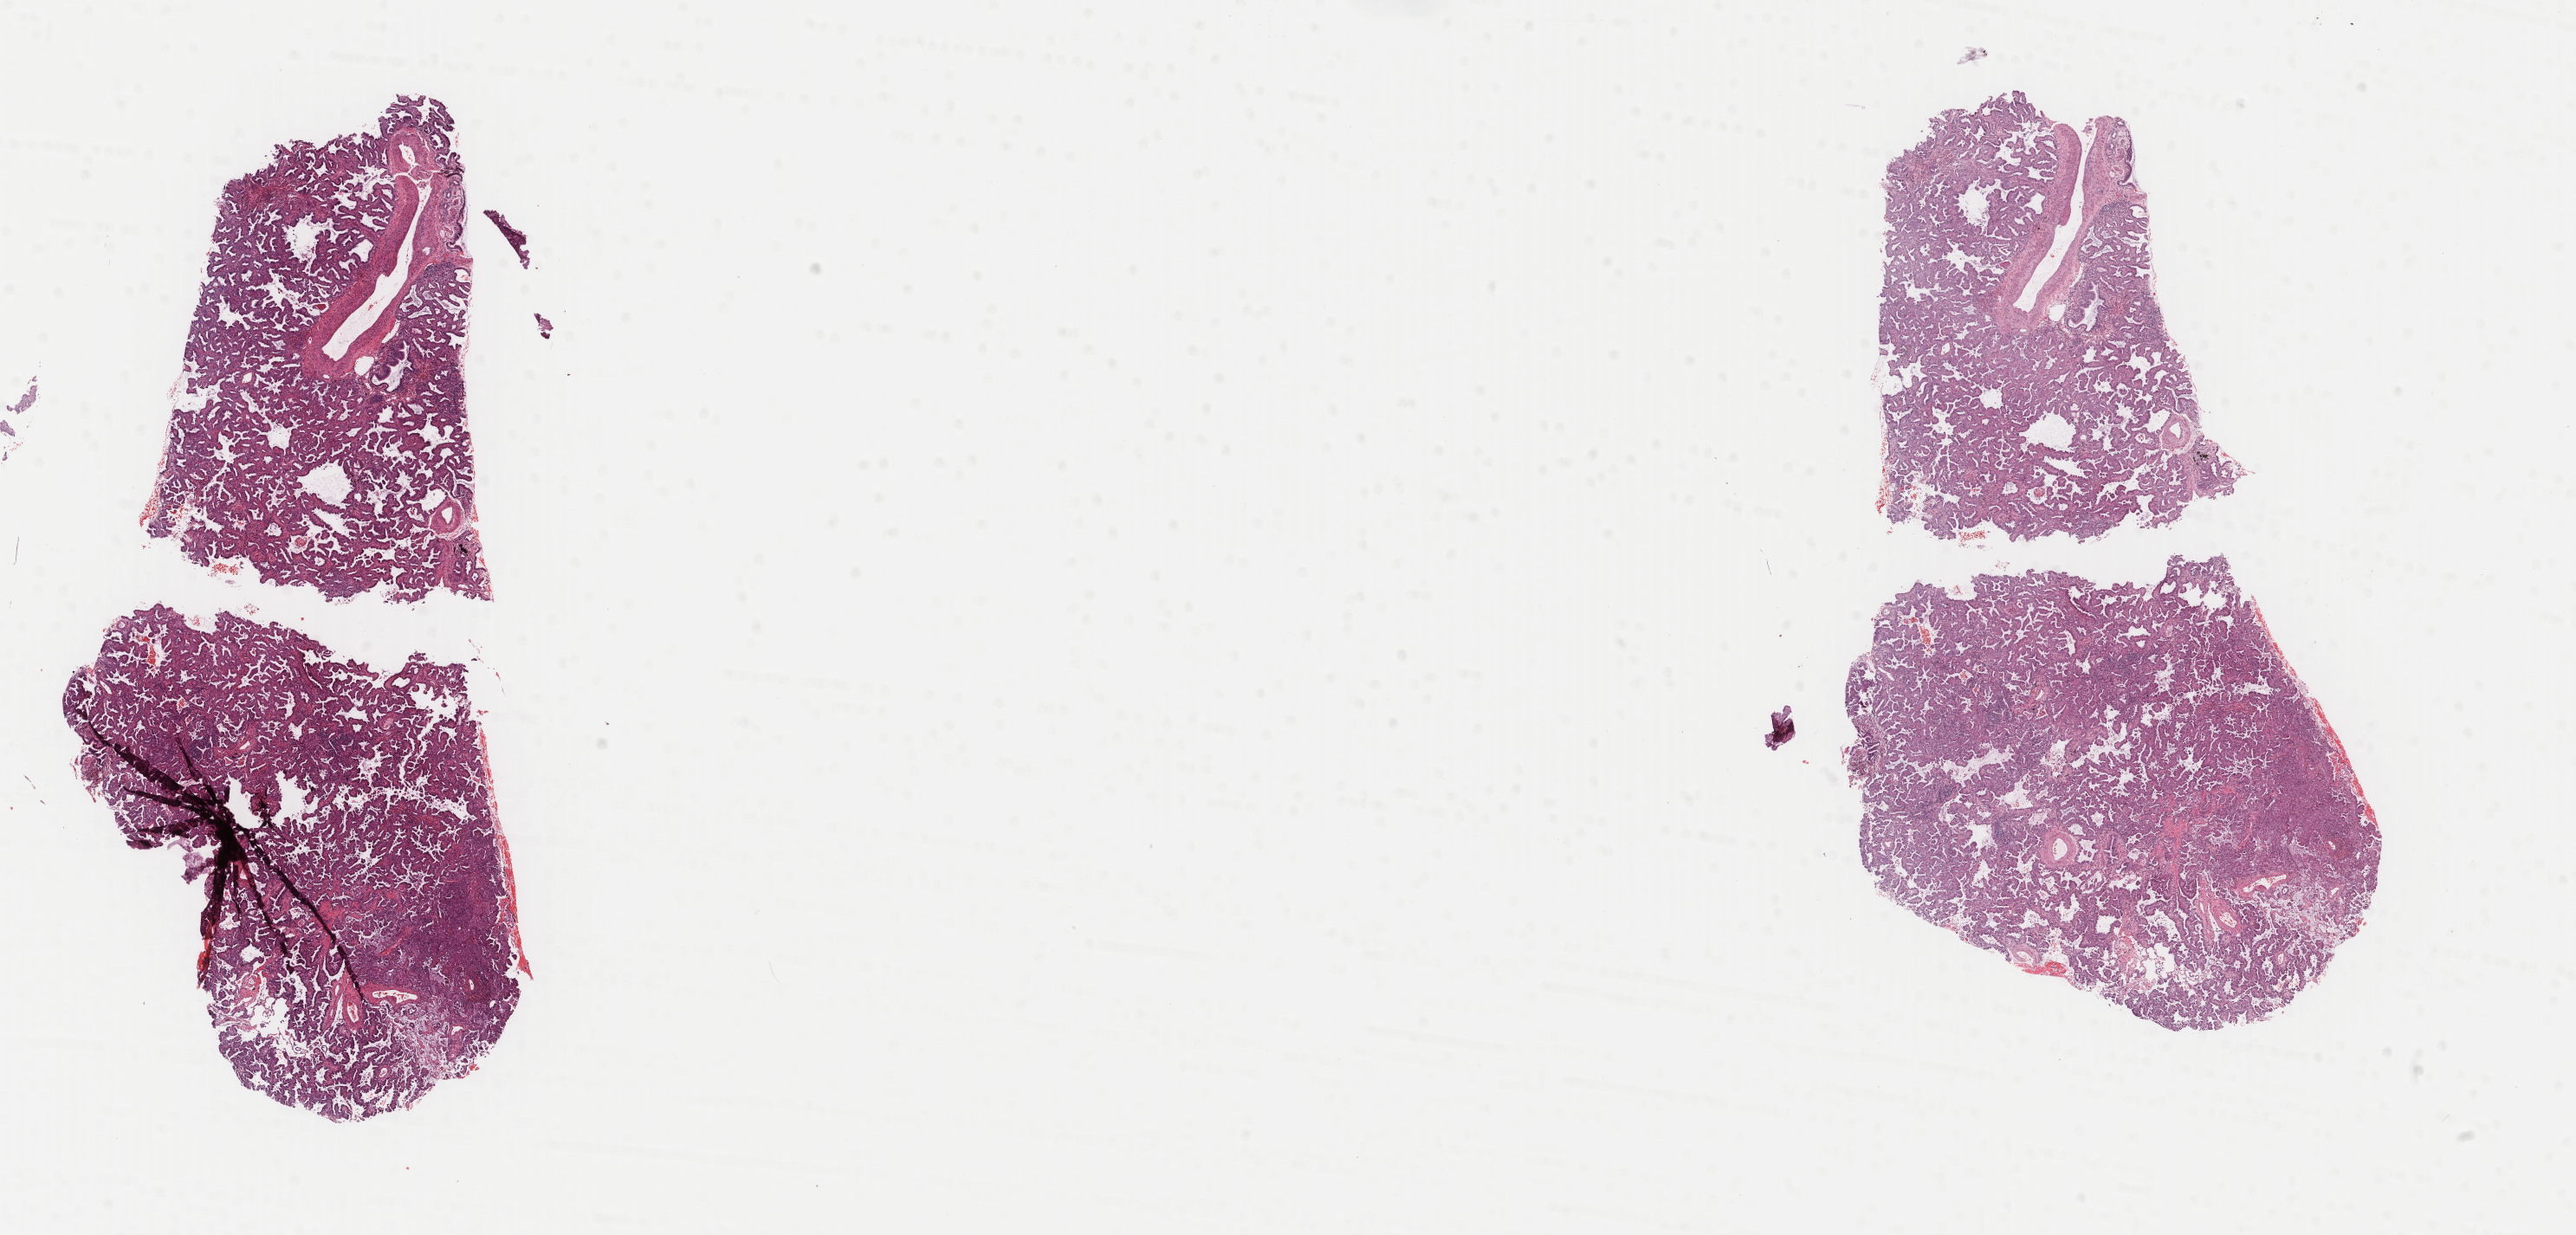
Whole-slide histology image, H&E-stained, a low-resolution overview of the entire scanned area, about 23.6 x 11.3 mm (from a 40x scan), frozen section, lung, primary tumour sample. Male, age 43 years at initial diagnosis. Composition of this section per pathologist review: tumour cells 70%, tumour nuclei 80%, normal cells 0%, stromal cells 25%, necrosis 5%. Infiltration values recorded for this section: lymphocyte infiltration 0%, monocyte infiltration 0%, neutrophil infiltration 0%.
Pathologic diagnosis: Adenocarcinoma, NOS (upper lobe, lung). AJCC pathologic stage: IB.